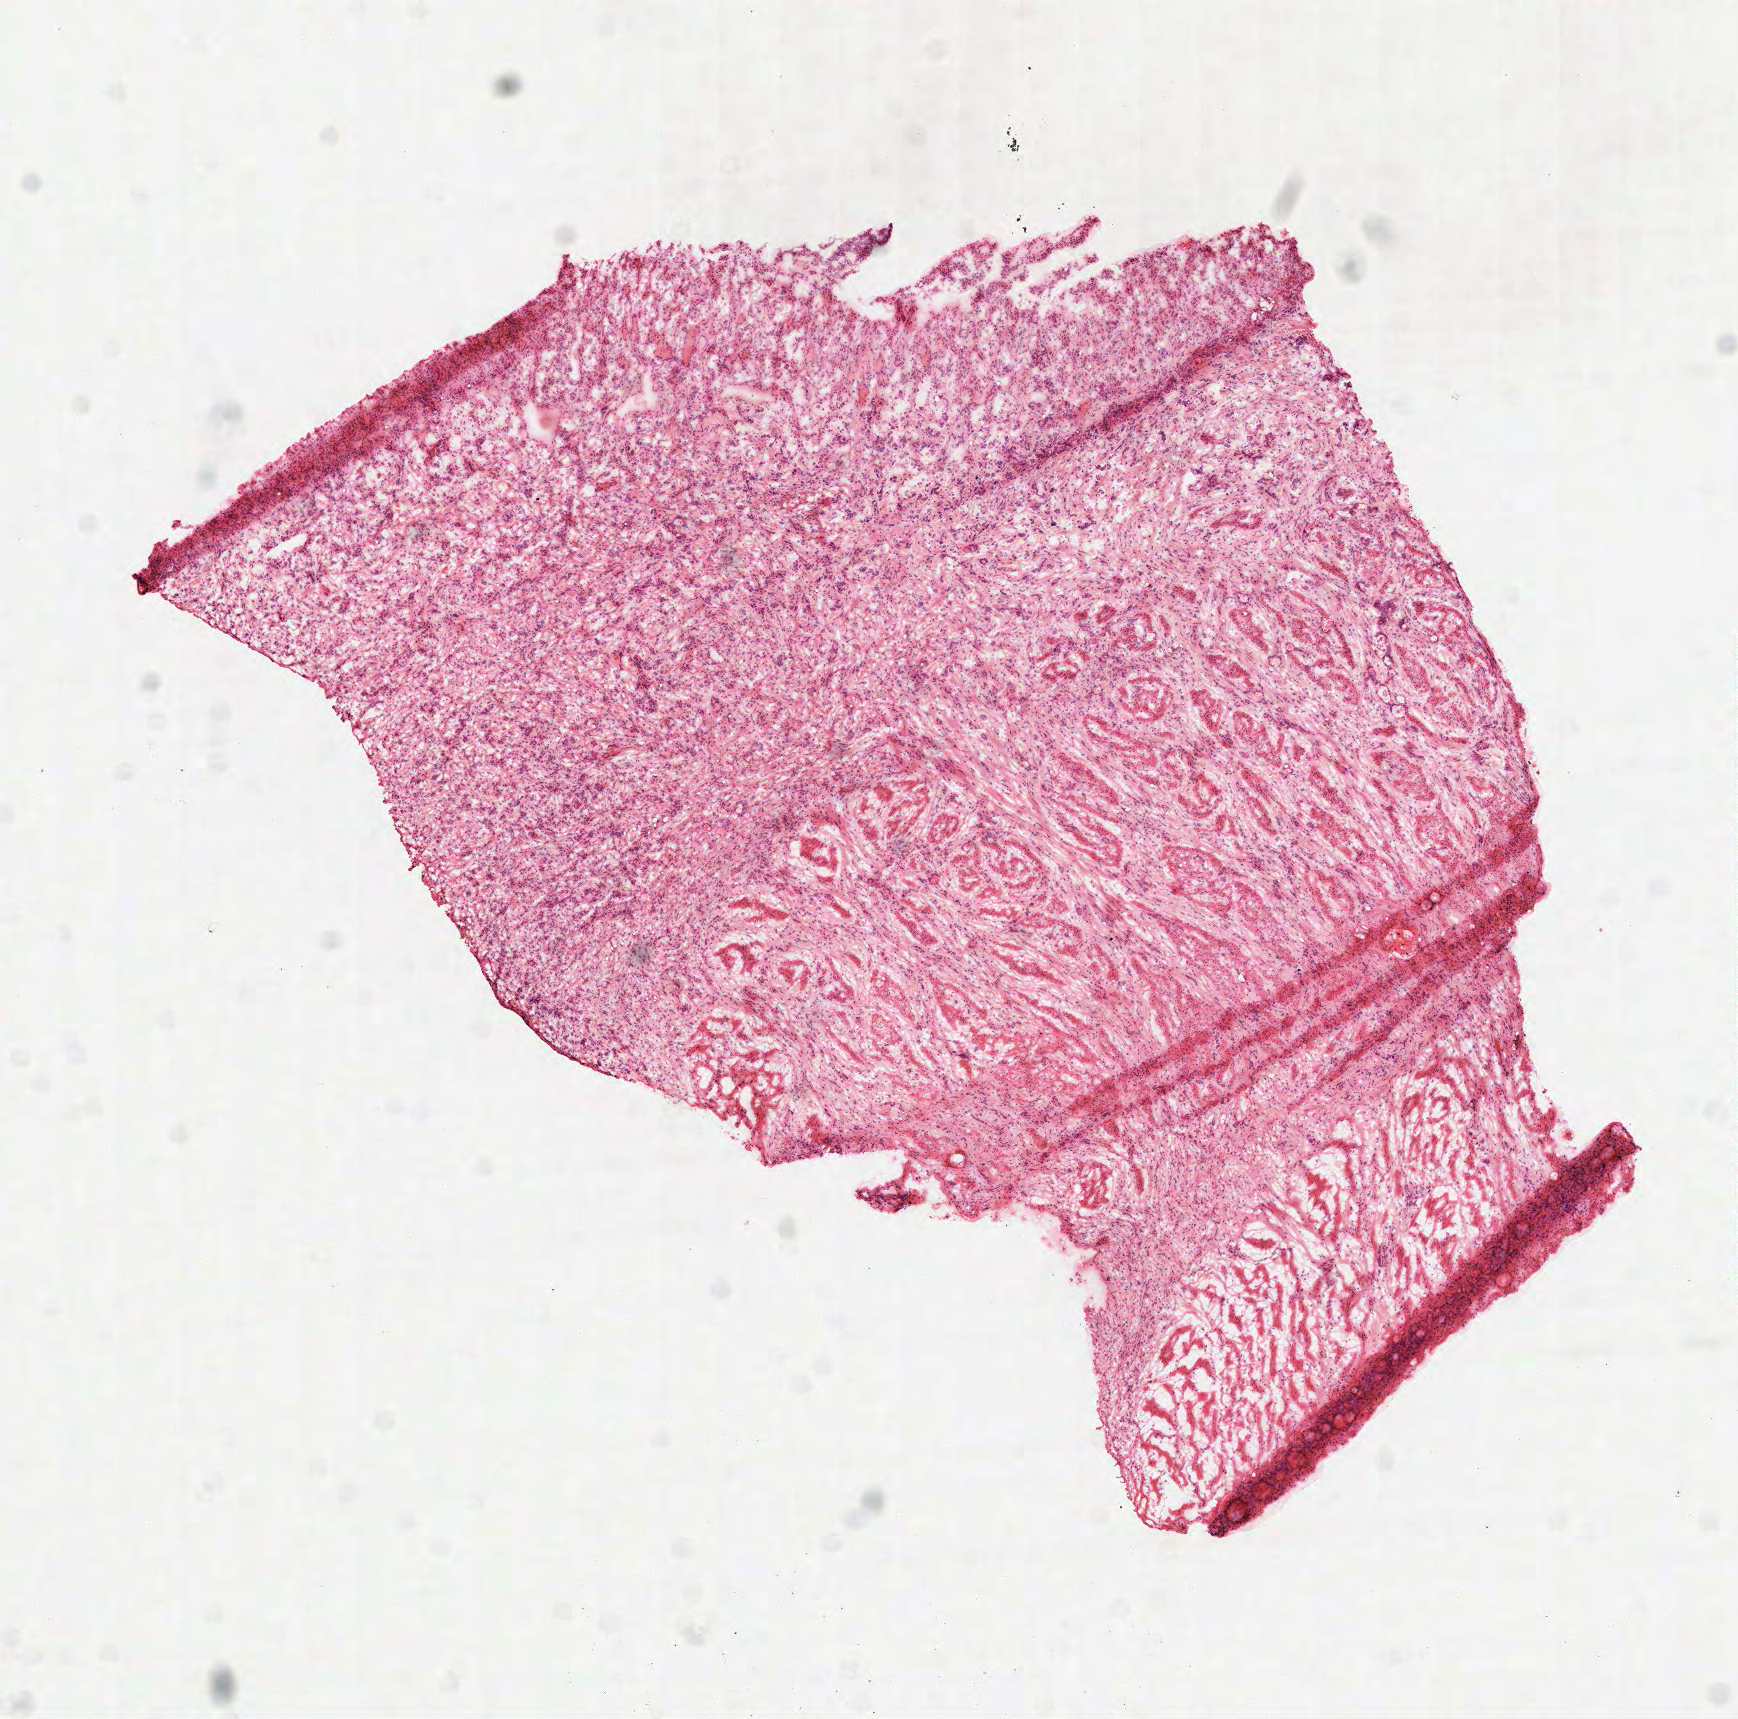
Whole-slide histology image, H&E-stained — a low-resolution overview of the entire scanned area, about 7.0 x 6.9 mm. Frozen section. Sample: primary tumour, stomach. Male patient; age at initial diagnosis 75 years. Histologic grade: G3 (poorly differentiated). Composition of this section per pathologist review: tumour cells 80%, tumour nuclei 75%, normal cells 0%, stromal cells 20%, necrosis 0%.
Lymph nodes positive (case pathology): 17 of 20 examined. AJCC pathologic stage: IIIA (7th edition). Diagnosis: Carcinoma, diffuse type (cardia, NOS).